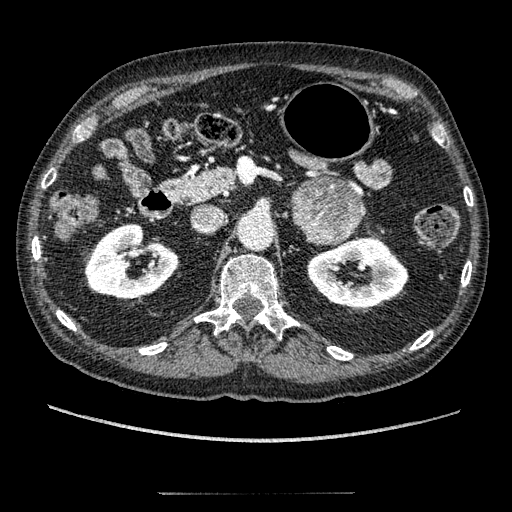
Contrast-enhanced abdominal CT, one axial slice; position 115 of 274 along the scan axis; reconstruction kernel STANDARD; 120 kVp; intravenous contrast given; soft-tissue window (W 400 / L 40 HU); 1.25 mm slice thickness; 512 × 512 image matrix. Male patient, age 69 years. Case-level facts recorded for this patient, not image findings: diagnosis: adrenocortical carcinoma; tumour side: left adrenal; tumour size at pathology: 6.1 cm; Ki-67 index: 10 %; stage (as recorded): 3.
Structures marked on this image (semi-automatically segmented with operator editing):
- mass: box from (x=292, y=178) to (x=364, y=243) px